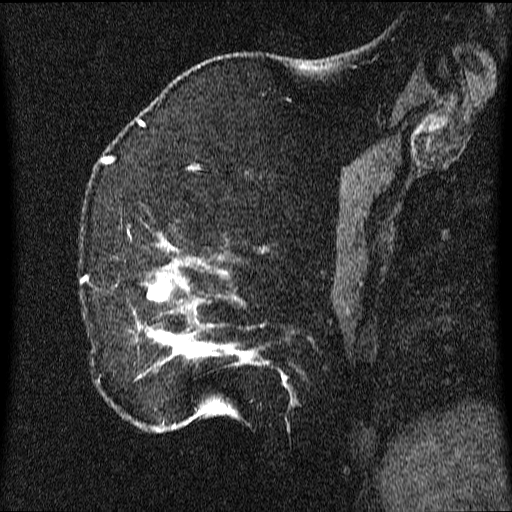
Breast MRI (dynamic contrast-enhanced), one sagittal slice. Dynamic contrast-enhanced series, image 2 of 3 at this slice position (ordered by acquisition). 1.5 T. TE 4.2 ms, TR 9.1 ms. 2.2 mm slice thickness. 512 × 512 image matrix, field of view 180 × 180 mm. Female patient, age 52 years.
Structures marked on this image (semi-automatic segmentation, software-assisted and operator-edited):
- analysis volume of interest (the breast-tissue region the enhancement analysis was run in; not a lesion): bounding box <81,204,347,433> (left, top, right, bottom; pixels)
- tumour enhancement mask (voxels above the 70 % enhancement threshold inside the analysis volume of interest): <84,232,288,430>